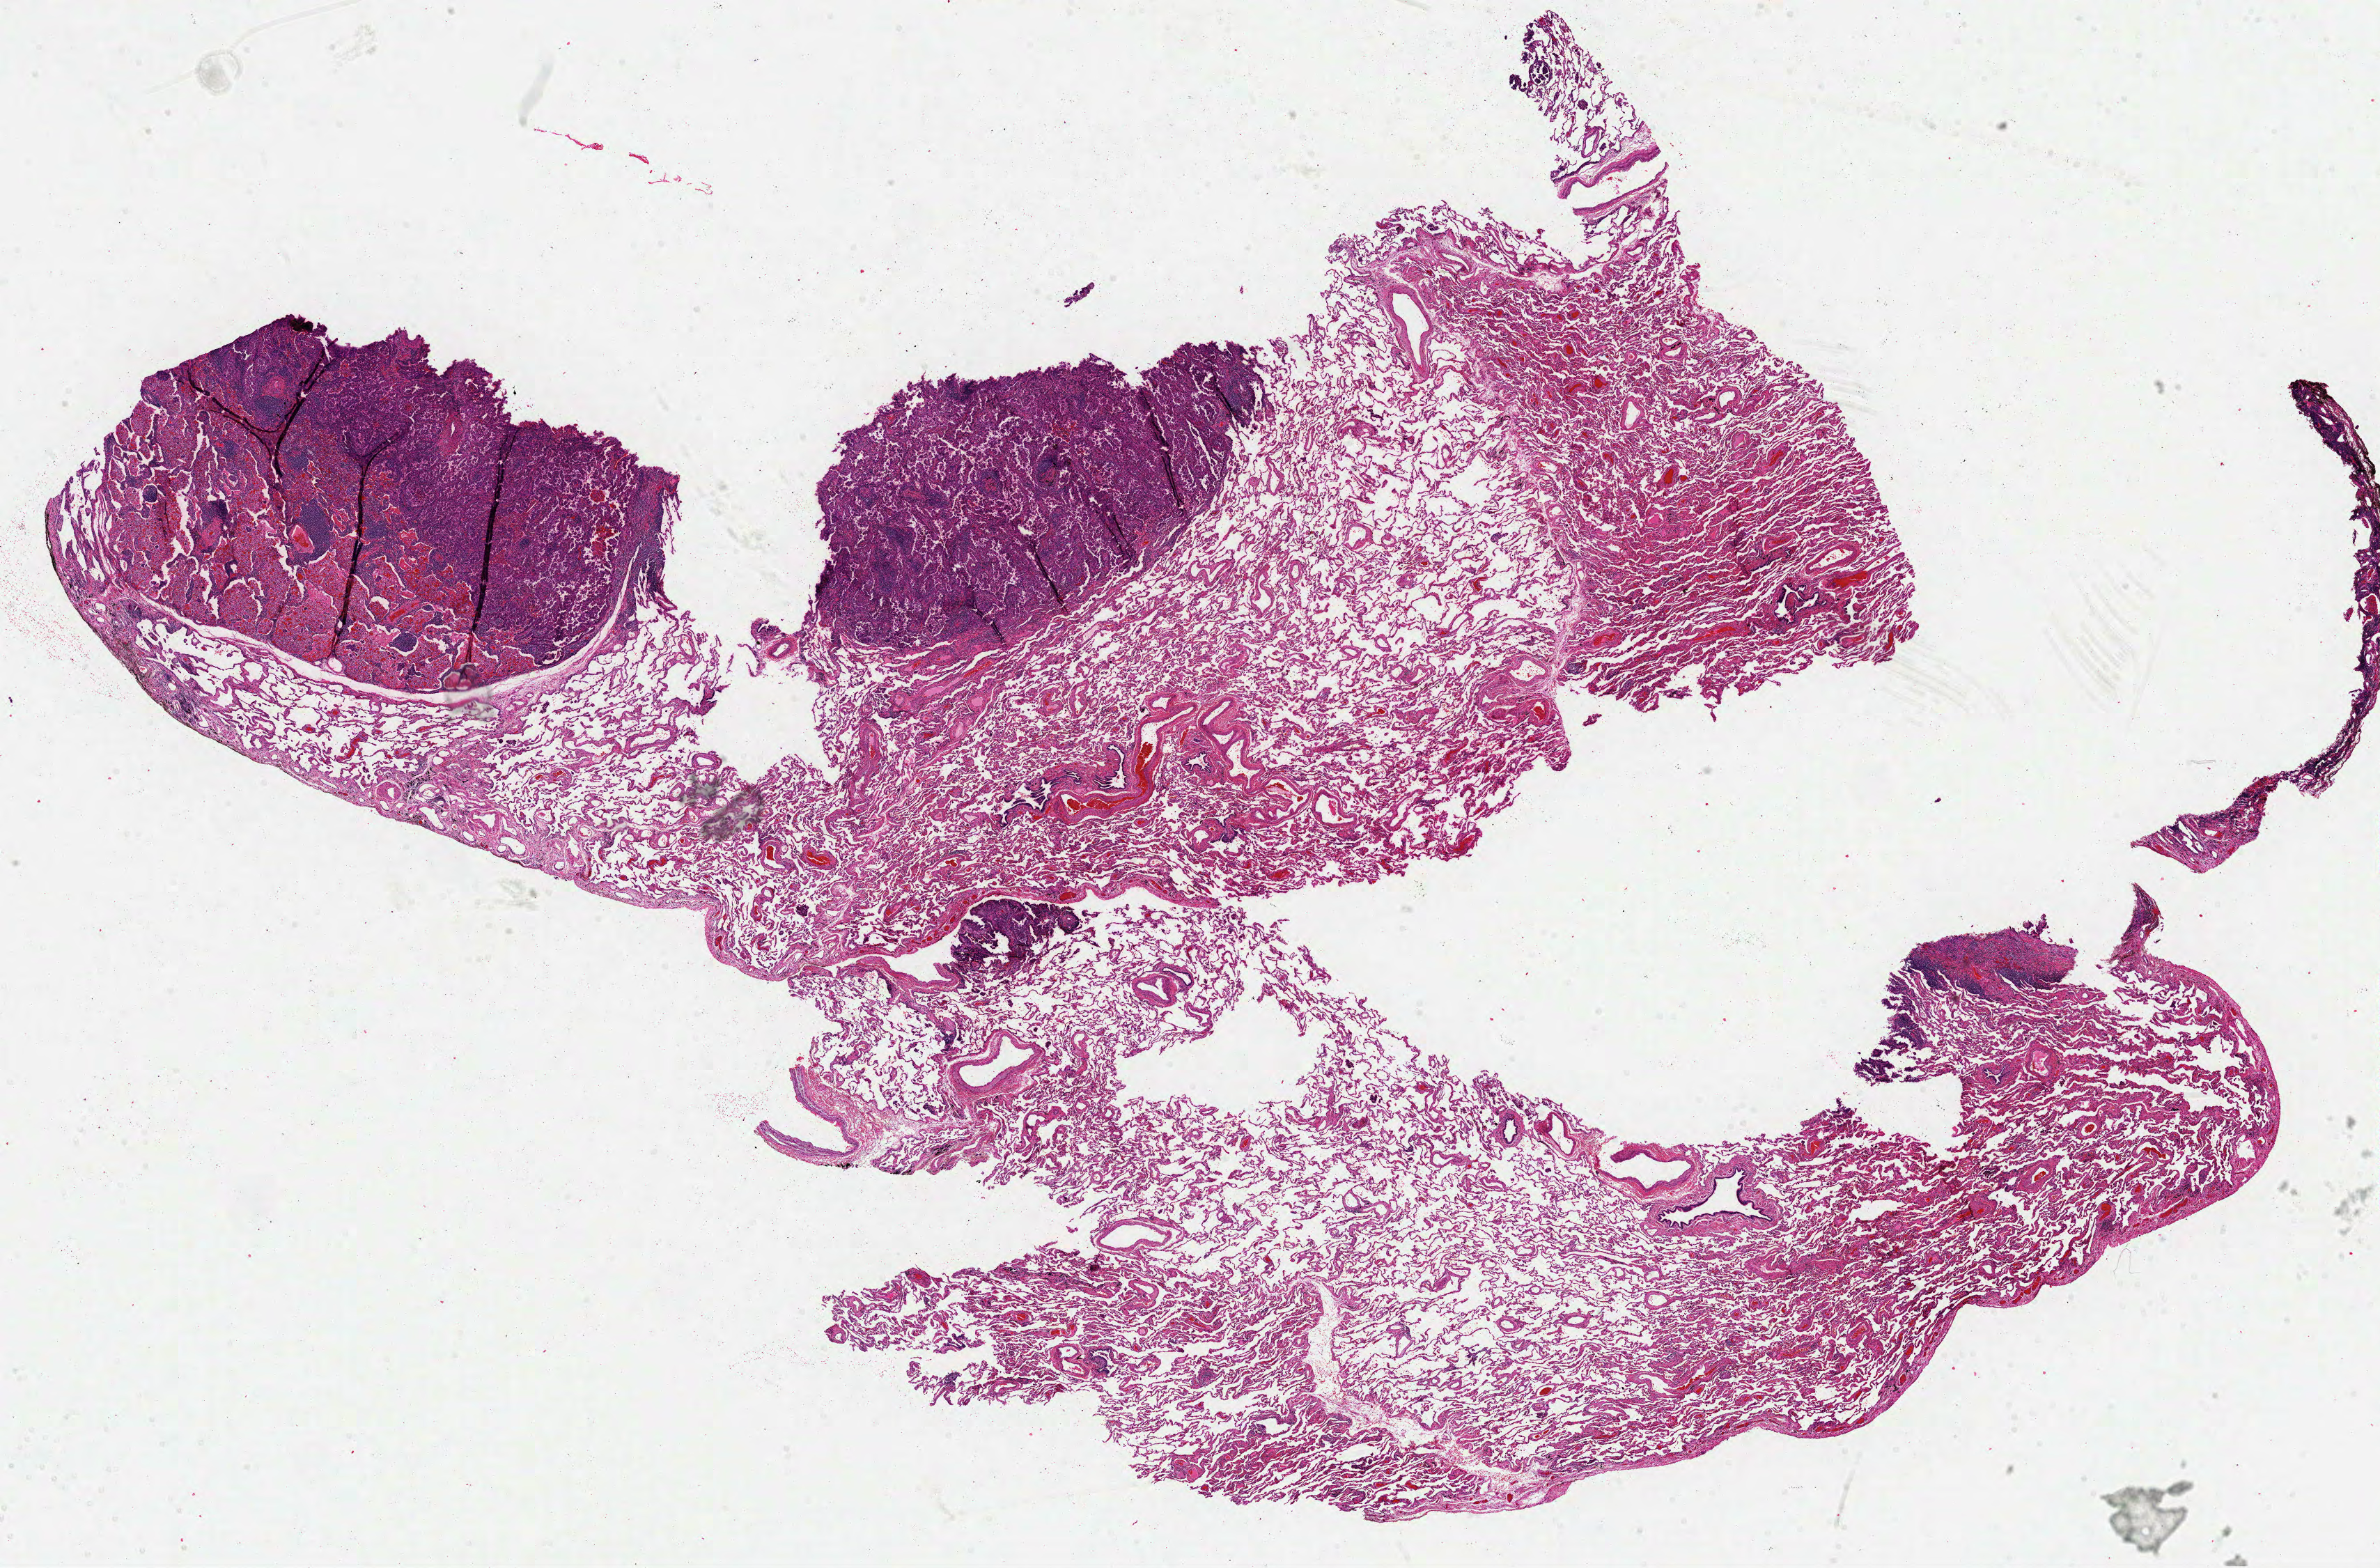
Digitized H&E tissue section (whole slide), shown as a low-resolution overview of the whole scanned area (about 27.6 x 18.2 mm, from a 40x scan). FFPE section. Primary tumour sample from the lung. Patient: female, age at initial diagnosis 74 years.
AJCC pathologic stage: IA (3rd edition). TNM: T1 N0 MX. Histologic diagnosis: Adenocarcinoma, NOS.